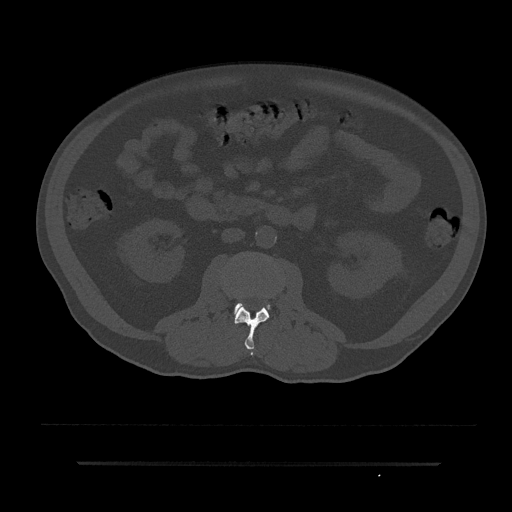
CT including the spine, one axial slice; position 45 of 797 along the scan axis; reconstruction kernel Br40s/3; 120 kVp; bone window (W 1800 / L 400 HU); 0.5 mm slice thickness; 512 × 512 image matrix, field of view 464 × 464 mm. Patient: male, 59 years. Case-level facts recorded for this patient, not image findings: primary cancer: bile ducts; vertebrae with lytic lesions (as recorded): T10.
Structures marked on this image (semi-automatic segmentation, software-assisted and operator-edited):
- L2 vertebra: bounding box [x1, y1, x2, y2] px = [235, 305, 269, 356]
- L3 vertebra: [235, 303, 269, 311]